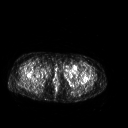
FDG PET of an extremity soft-tissue mass (from a PET/CT study), one axial slice. Slice 255 of 267 in the series (ordered by position). 3.27 mm slice thickness. 128 × 128 image matrix, field of view 500 × 500 mm. Patient: female, 42 years. Case-level facts recorded for this patient, not image findings: histological type: pleiomorphic leiomyosarcoma; grade: intermediate; site of the primary tumour: left thigh.
Outlined on this slice (expert contour drawn on MRI and transferred to this co-registered scan by the dataset authors):
- gross tumour volume including surrounding oedema: bounding box (x1, y1, x2, y2) in pixels: (61, 64, 79, 77)
- gross tumour volume (mass): (66, 65, 79, 77)